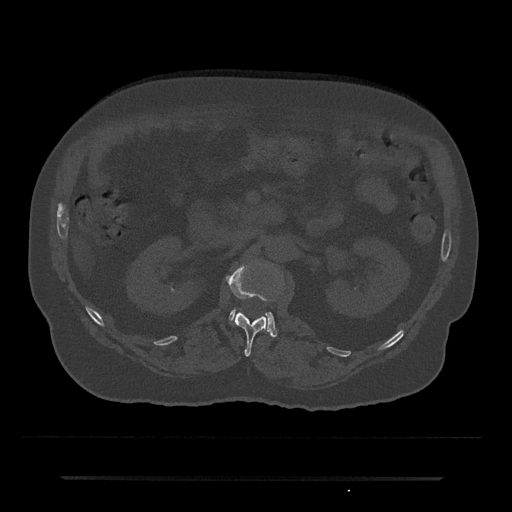
CT including the spine, one axial slice; slice 50 of 797 in the series (ordered by position); reconstruction kernel Br40s/3; 120 kVp; bone window (W 1800 / L 400 HU); 0.5 mm slice thickness; 512 × 512 image matrix, field of view 437 × 437 mm. Male patient, age 69 years. Case-level facts recorded for this patient, not image findings: primary cancer: prostate.
Annotated regions visible in this slice (semi-automatic segmentation, software-assisted and operator-edited):
- L1 vertebra: bounding box (x1, y1, x2, y2) in pixels: (226, 262, 271, 356)
- L2 vertebra: (229, 309, 277, 337)